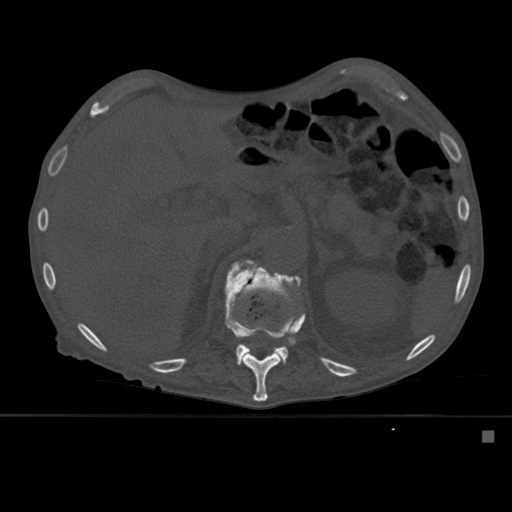
CT including the spine, one axial slice; bone window (W 1800 / L 400 HU); 512 × 512 image matrix. Patient: male, 78 years. Case-level facts recorded for this patient, not image findings: primary cancer: prostate.
Outlined on this slice (semi-automatic segmentation, software-assisted and operator-edited):
- L1 vertebra: bounding box <235,264,294,365> (left, top, right, bottom; pixels)
- T12 vertebra: <225,259,305,401>